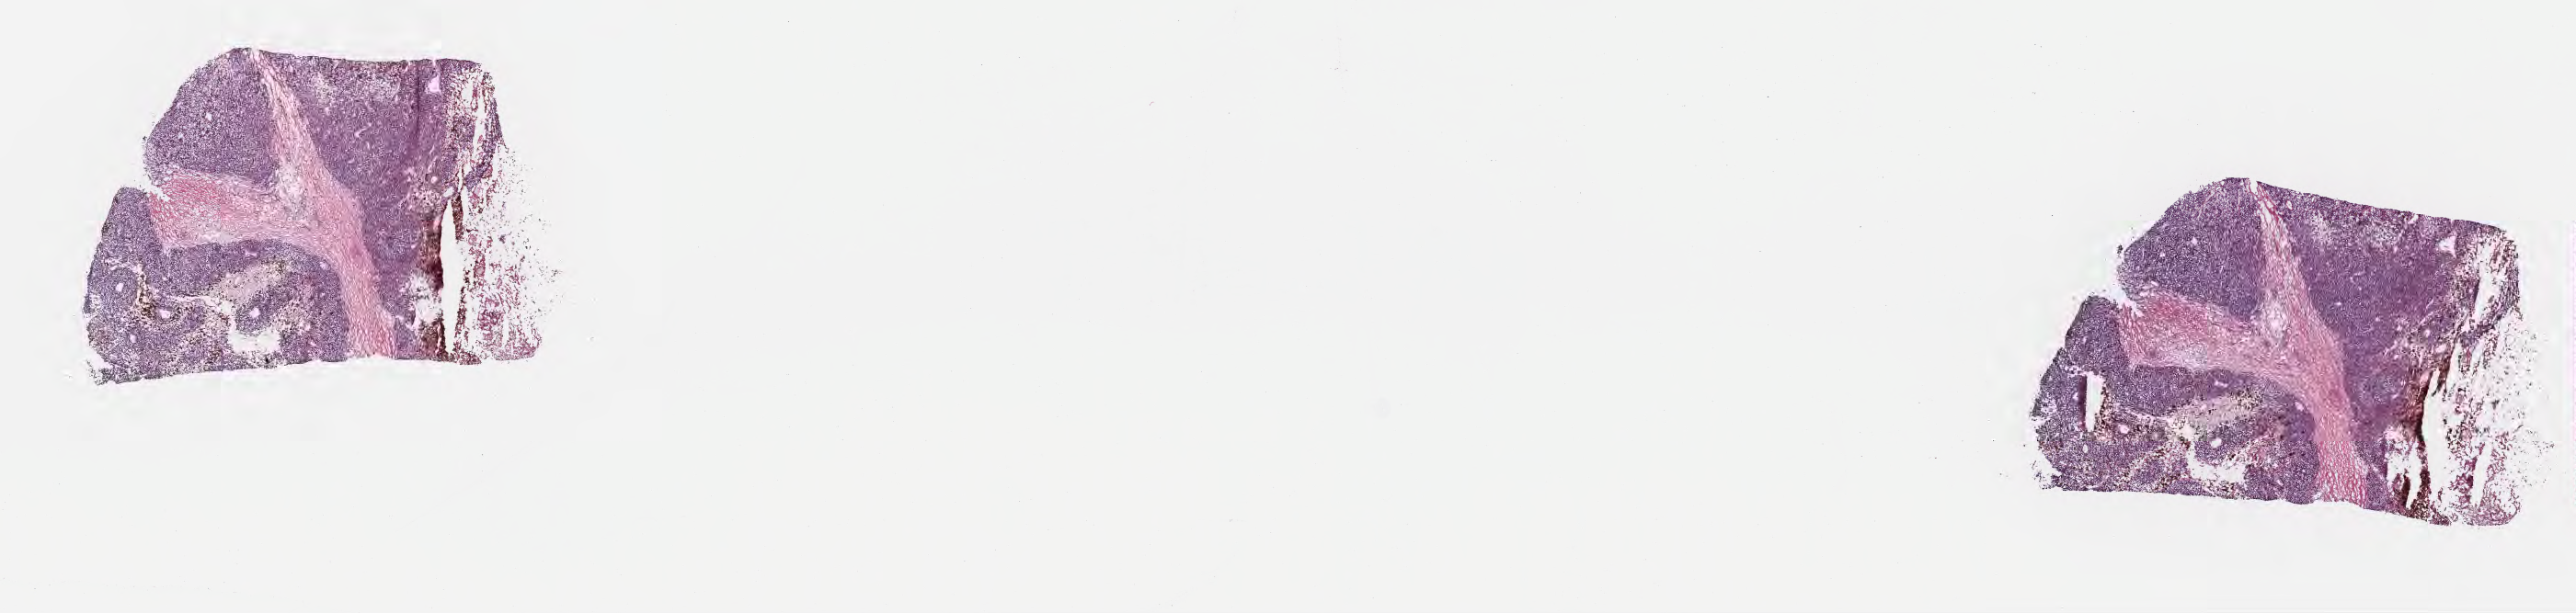
Whole-slide image, haematoxylin and eosin stain, whole scanned area (about 22.7 x 5.4 mm) shown as a low-resolution overview. Frozen section. Specimen: metastatic tumor tissue, resected from lymph nodes of axilla or arm. Male, age 63 years at initial diagnosis. Composition of this section per pathologist review: tumor cells 50%, tumor nuclei 60%, stromal cells 0%, necrosis 25%, normal cells 25%. Infiltration values recorded for this section: lymphocyte infiltration 0%, monocyte infiltration 0%, neutrophil infiltration 0%.
Patient diagnosis (primary): Malignant melanoma, NOS. Section: top of the tissue portion.